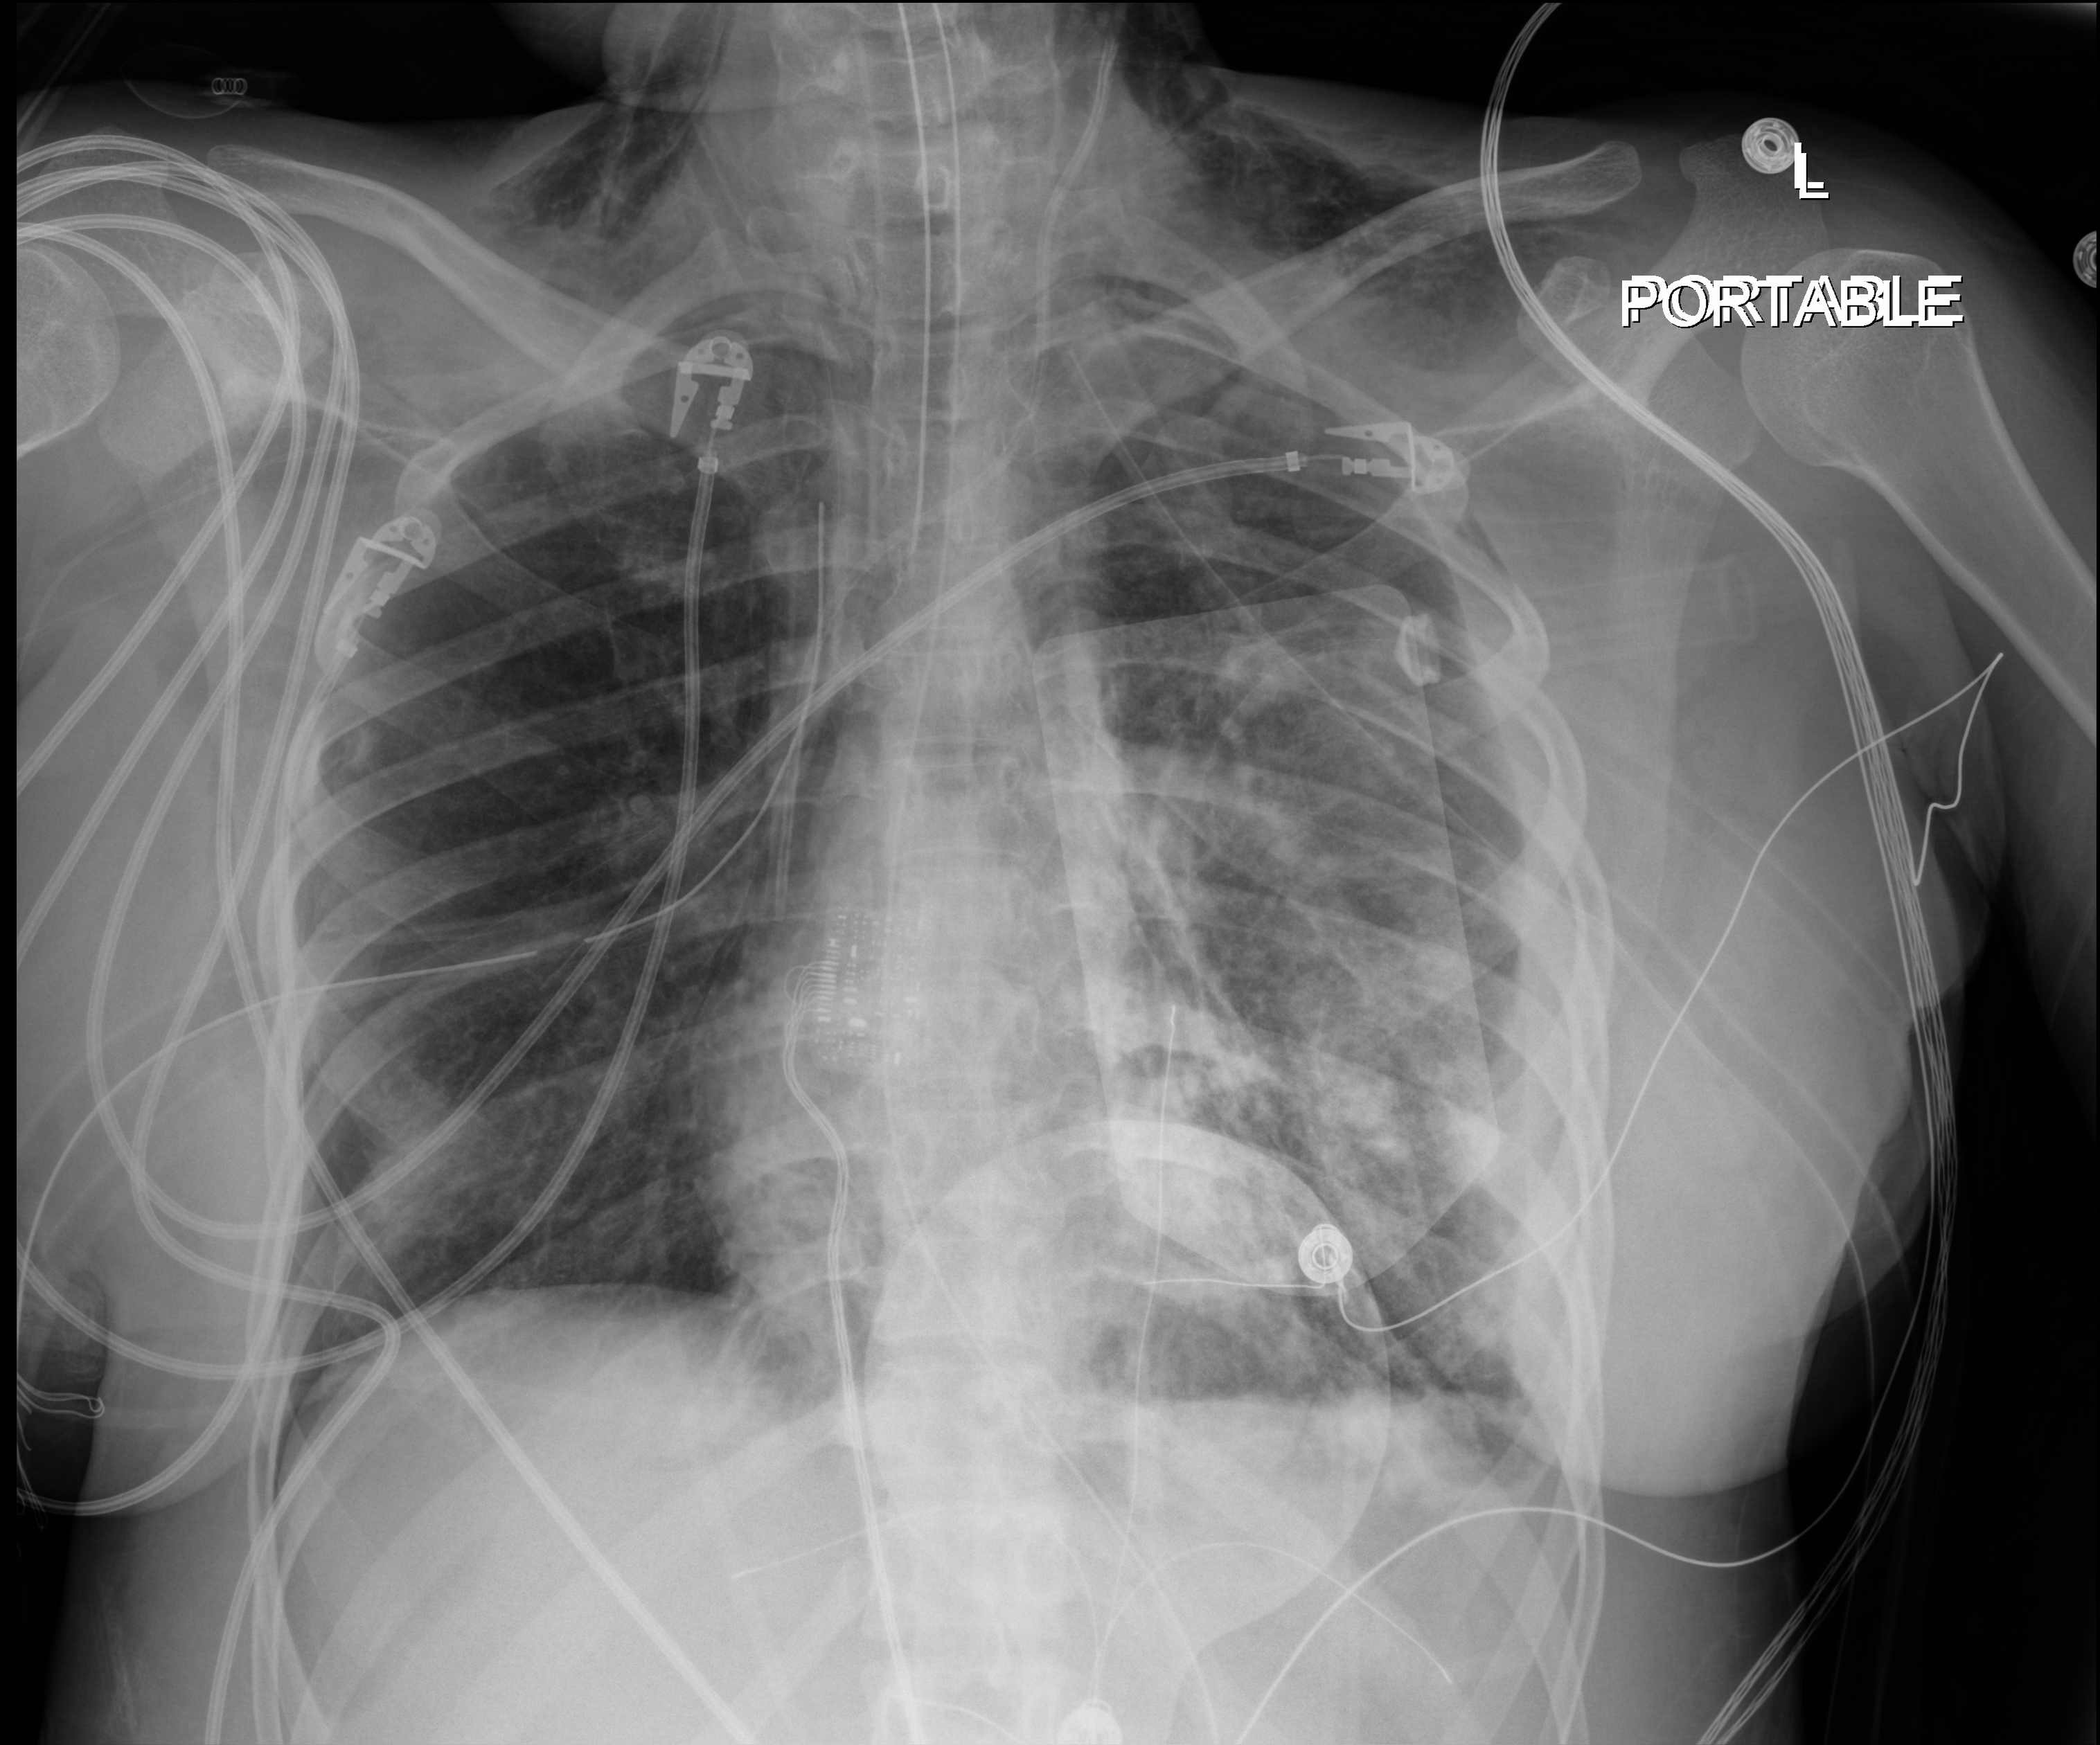
Portable chest radiograph; anteroposterior (AP) projection. Adult patient hospitalised with COVID-19, age 18–59 years.
From the hospital-stay record, not from the radiograph (when in the stay this image was taken is not recorded): length of hospital stay: 30 days; mechanically ventilated during this hospital stay: yes; admitted to intensive care during this hospital stay: yes.